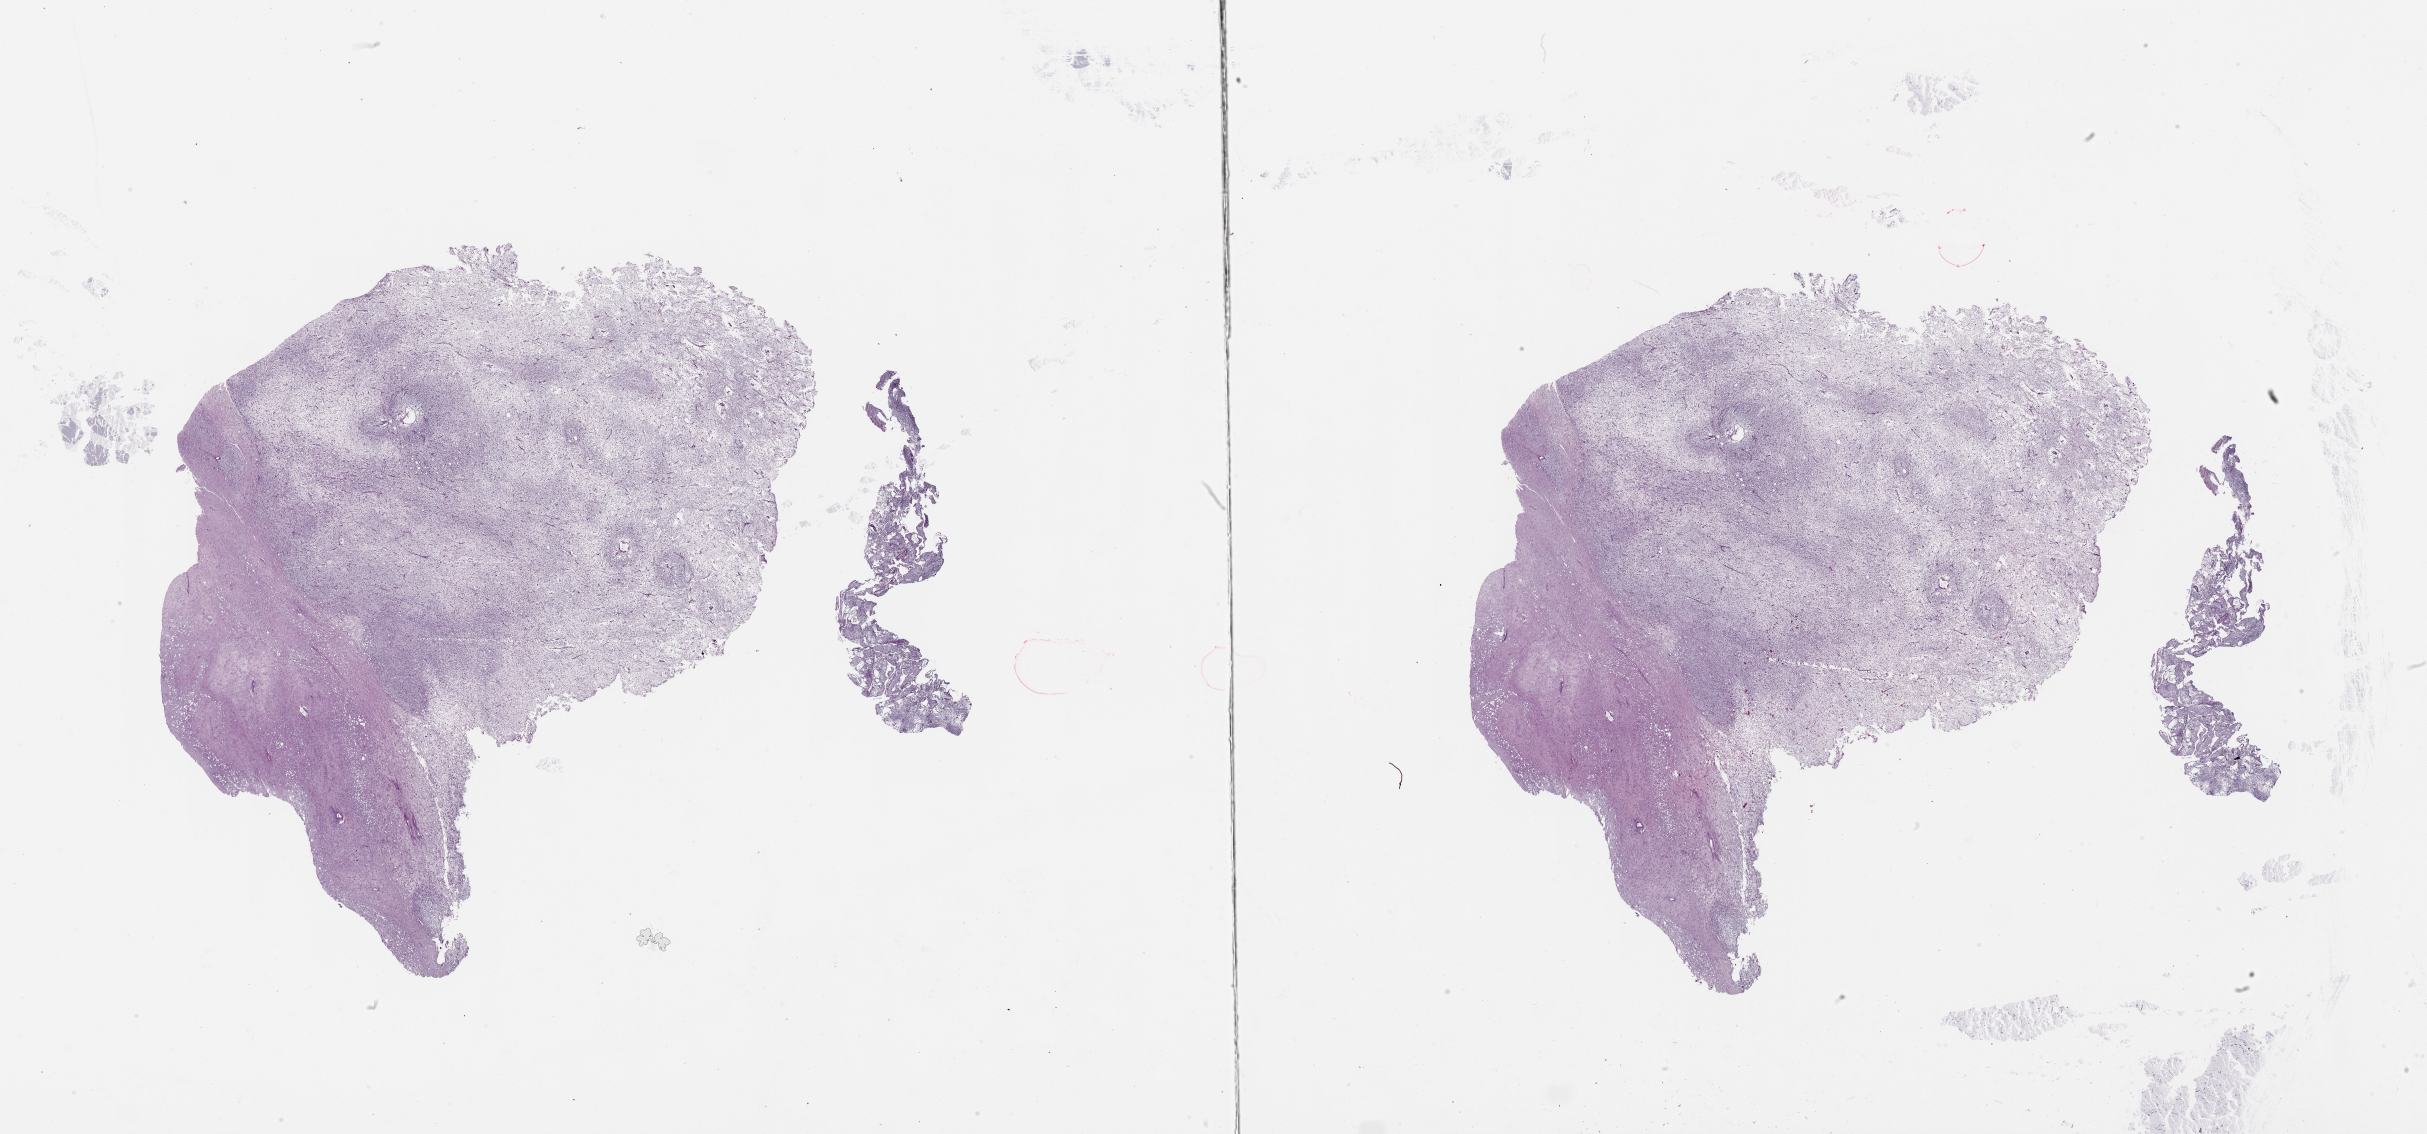
Digitized Hematoxylin and eosin (H&E) stained tissue section (whole slide), whole scanned area (about 39.1 x 18.3 mm, acquisition: 20x scan) shown as a low-resolution overview. Tumour tissue sample. Female, 78 y/o.
Primary tumour site (as recorded): lower extremity. Patient diagnosis (cohort enrolment): sarcoma (site not recorded at cohort level).